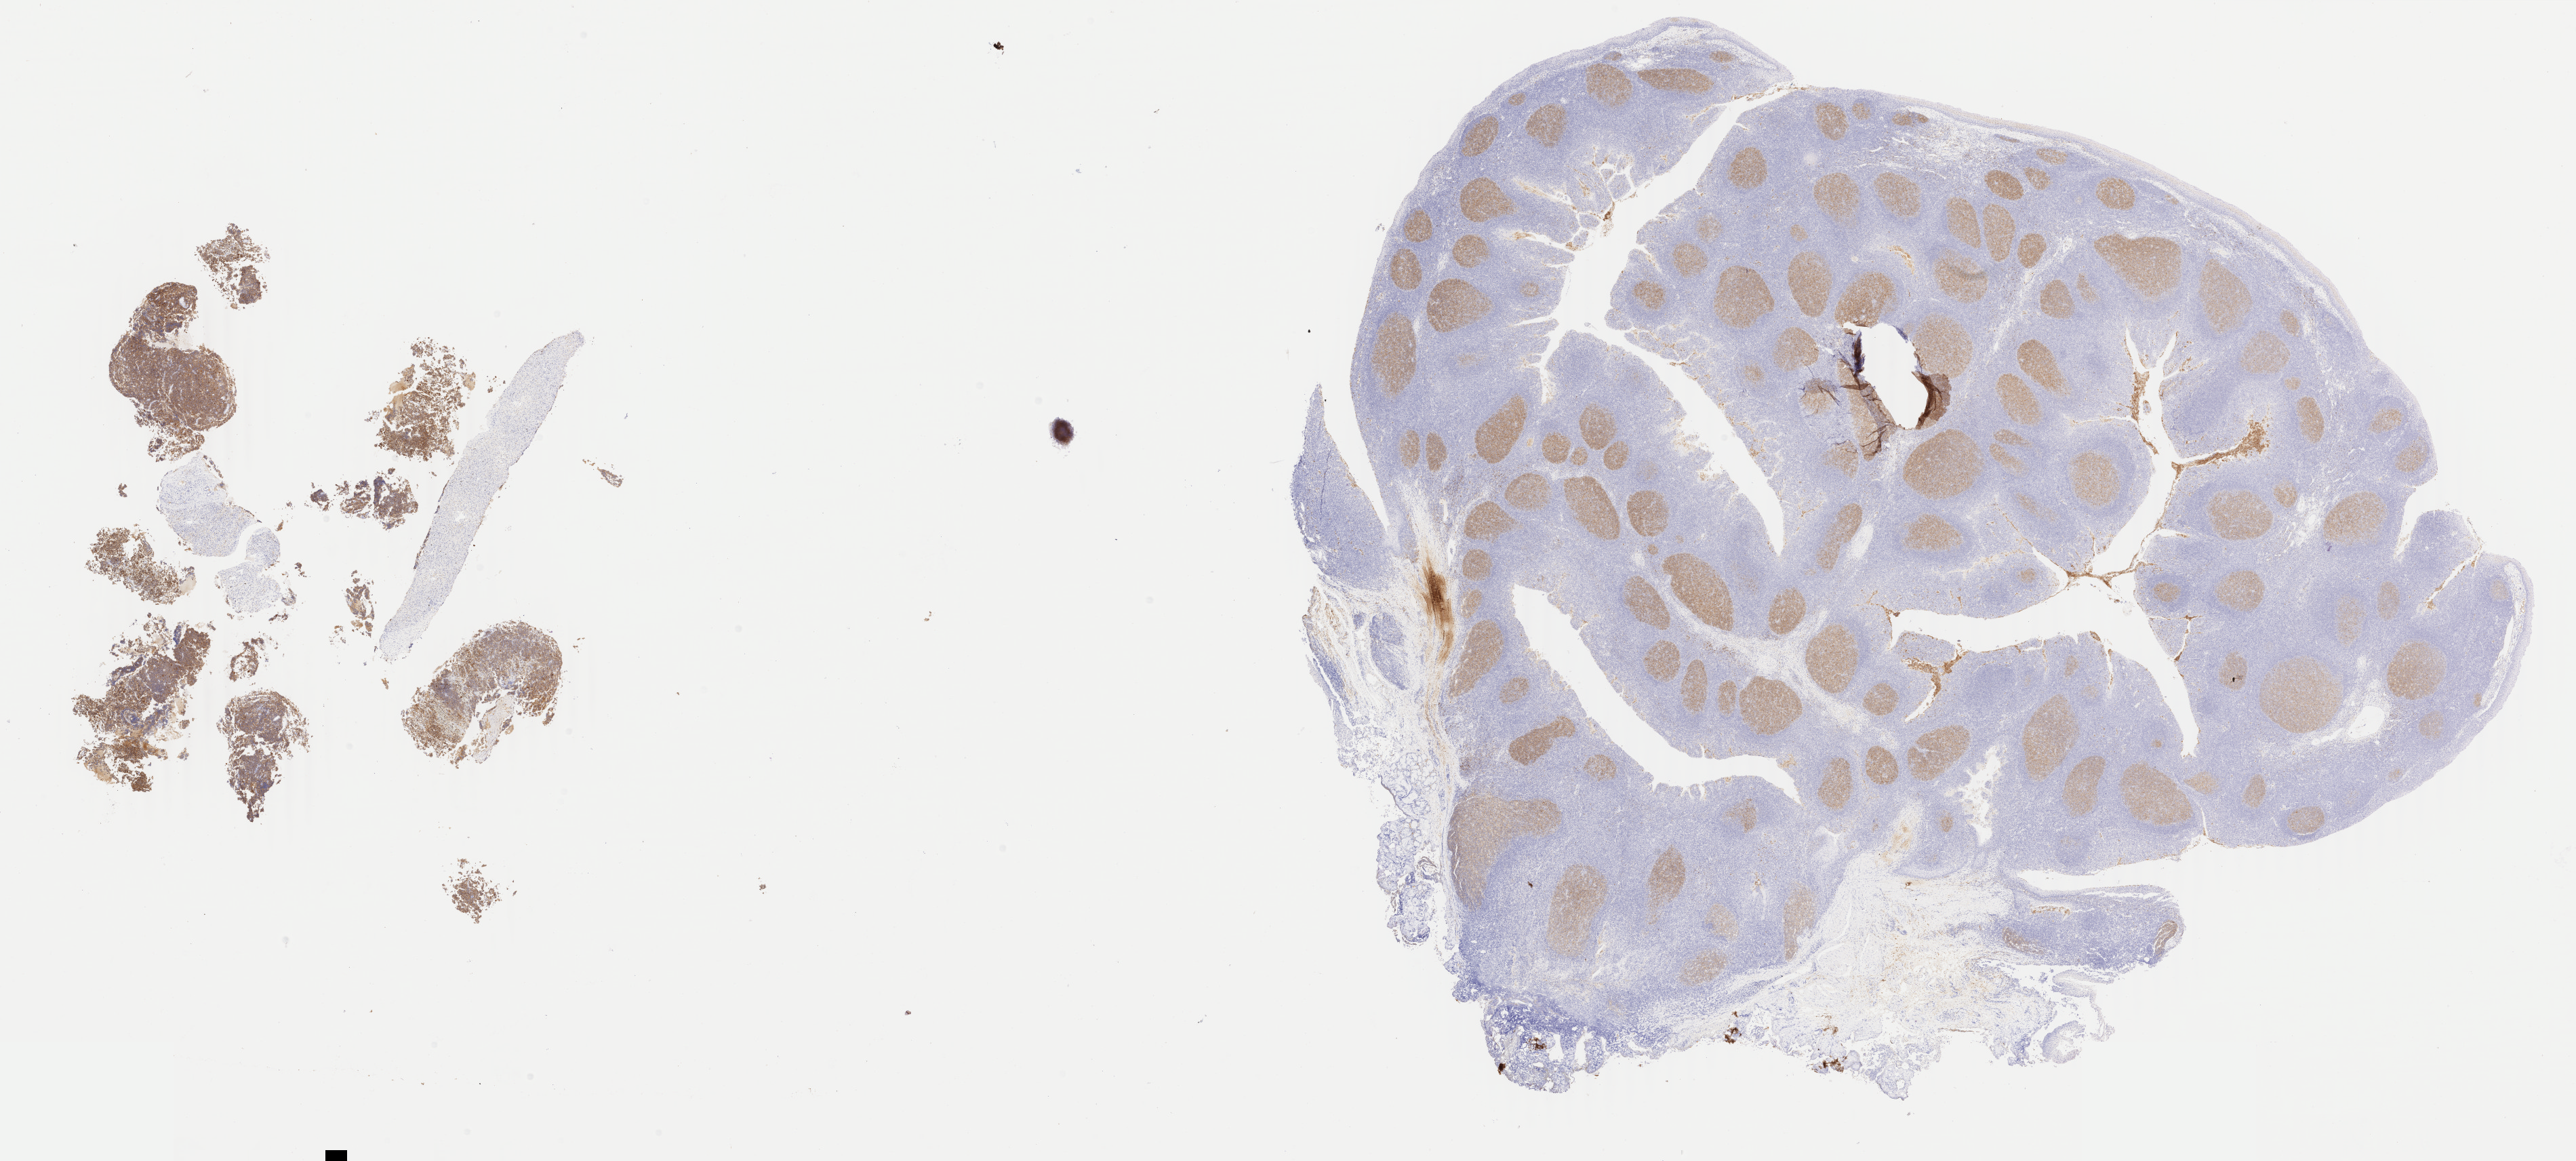
Immunohistochemistry (IHC) whole-slide image stained for CD10 — whole scanned area (about 30.2 x 13.6 mm) shown as a low-resolution overview. Tumor tissue. Anatomic site: liver. Male, age 5 years at initial diagnosis.
* histologic diagnosis: Burkitt lymphoma, NOS